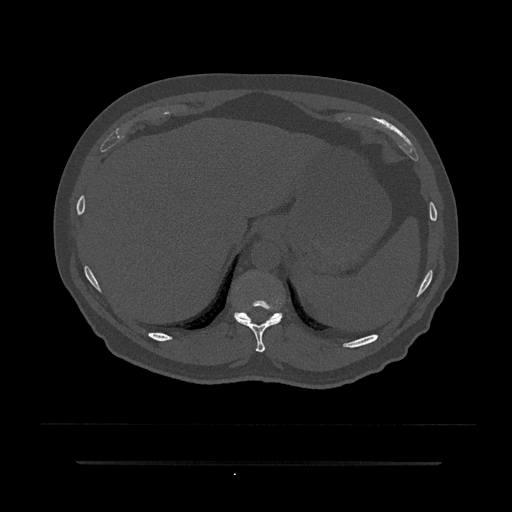
CT including the spine, one axial slice. Slice 305 of 797 in the series (ordered by position). 120 kVp. Bone window (W 1800 / L 400 HU). 0.5 mm slice thickness. 512 × 512 image matrix. Patient: male, 59 years. Case-level facts recorded for this patient, not image findings: primary cancer: bile ducts; vertebrae with lytic lesions (as recorded): T10.
Outlined on this slice (semi-automatically segmented with operator editing):
- T10 vertebra: bounding box (x1, y1, x2, y2) in pixels: (234, 295, 284, 353)
- T11 vertebra: (234, 312, 282, 323)